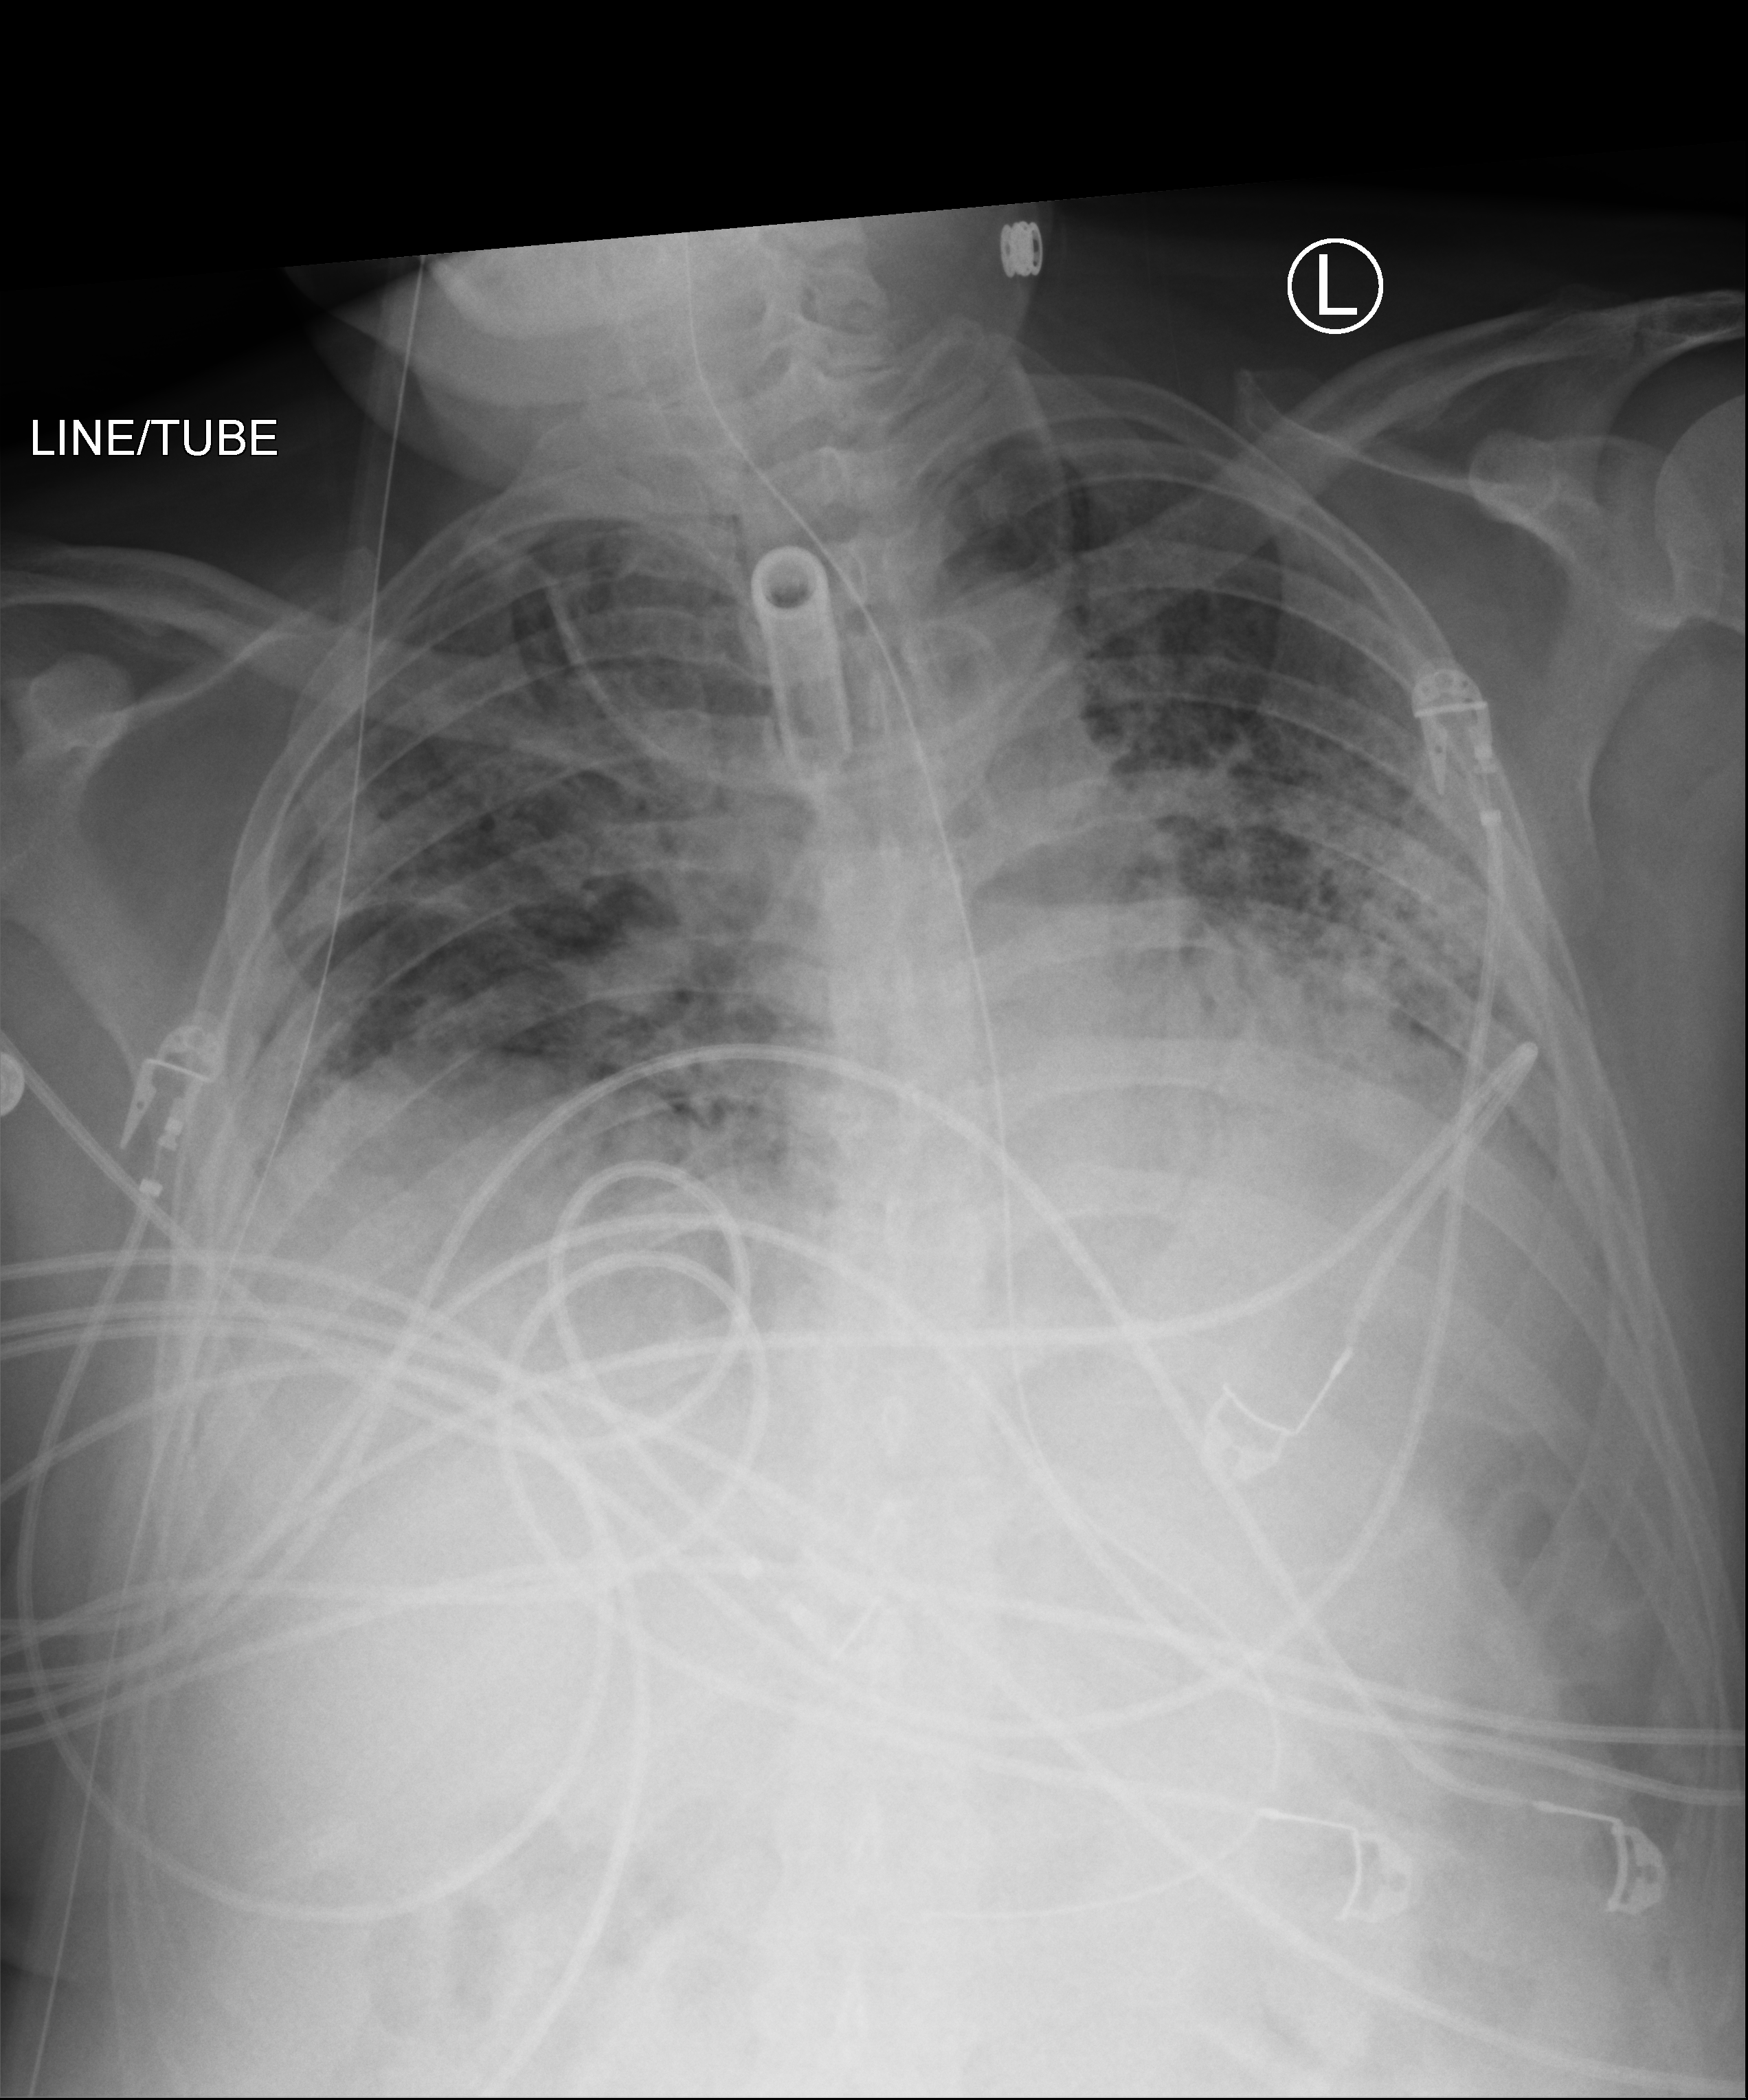
Portable chest radiograph, anteroposterior (AP) projection. Male patient hospitalised with COVID-19, age 18–59 years.
Hospital-stay facts (about this admission, not read from this image; timing relative to this image not recorded): hypertension (admission record): no; smoking status (admission record): never; admitted to intensive care during this hospital stay: yes.